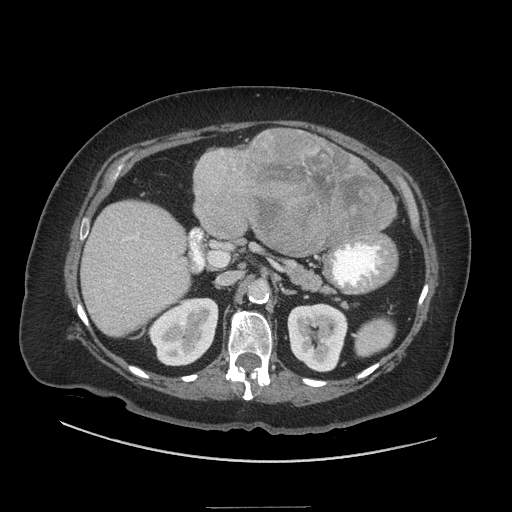
Contrast-enhanced abdominal CT (liver protocol), one axial slice; slice 16 of 81 in the series (ordered by position); soft-tissue window (W 400 / L 40 HU); 2.5 mm slice thickness; 512 × 512 image matrix, field of view 440 × 440 mm. From the clinical record (not read from this slice): diagnosis: hepatocellular carcinoma (patient treated with transarterial chemoembolisation; whether this scan precedes or follows treatment is not stated here); TNM stage (as recorded): Stage-II; Child-Pugh class: A; tumour differentiation: moderately differentiated; tumour nodularity: multinodular.
Structures marked on this image (semi-automatically segmented with operator editing):
- liver parenchyma outside the tumour (the mass and vessels are separate outlines, so this box may not span the whole liver): box from (x=80, y=132) to (x=388, y=336) px
- mass: (x=195, y=130)–(x=400, y=255)
- liver vessels: (x=108, y=233)–(x=167, y=303)